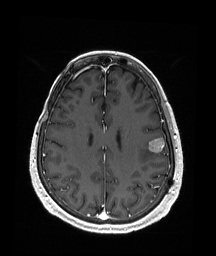
Brain MRI from a brain-tumour surgery series, one axial slice; position 70 of 176 along the scan axis; T1-weighted post-contrast; 1 mm slice thickness; 216 × 256 image matrix, field of view 211 × 250 mm. Case-level facts recorded for this patient, not image findings: histopathology: Metastatic Malignant Melanoma; tumour location: Left Frontal.
Structures marked on this image (manually delineated by an expert):
- tumour: box from (x=148, y=138) to (x=165, y=153) px